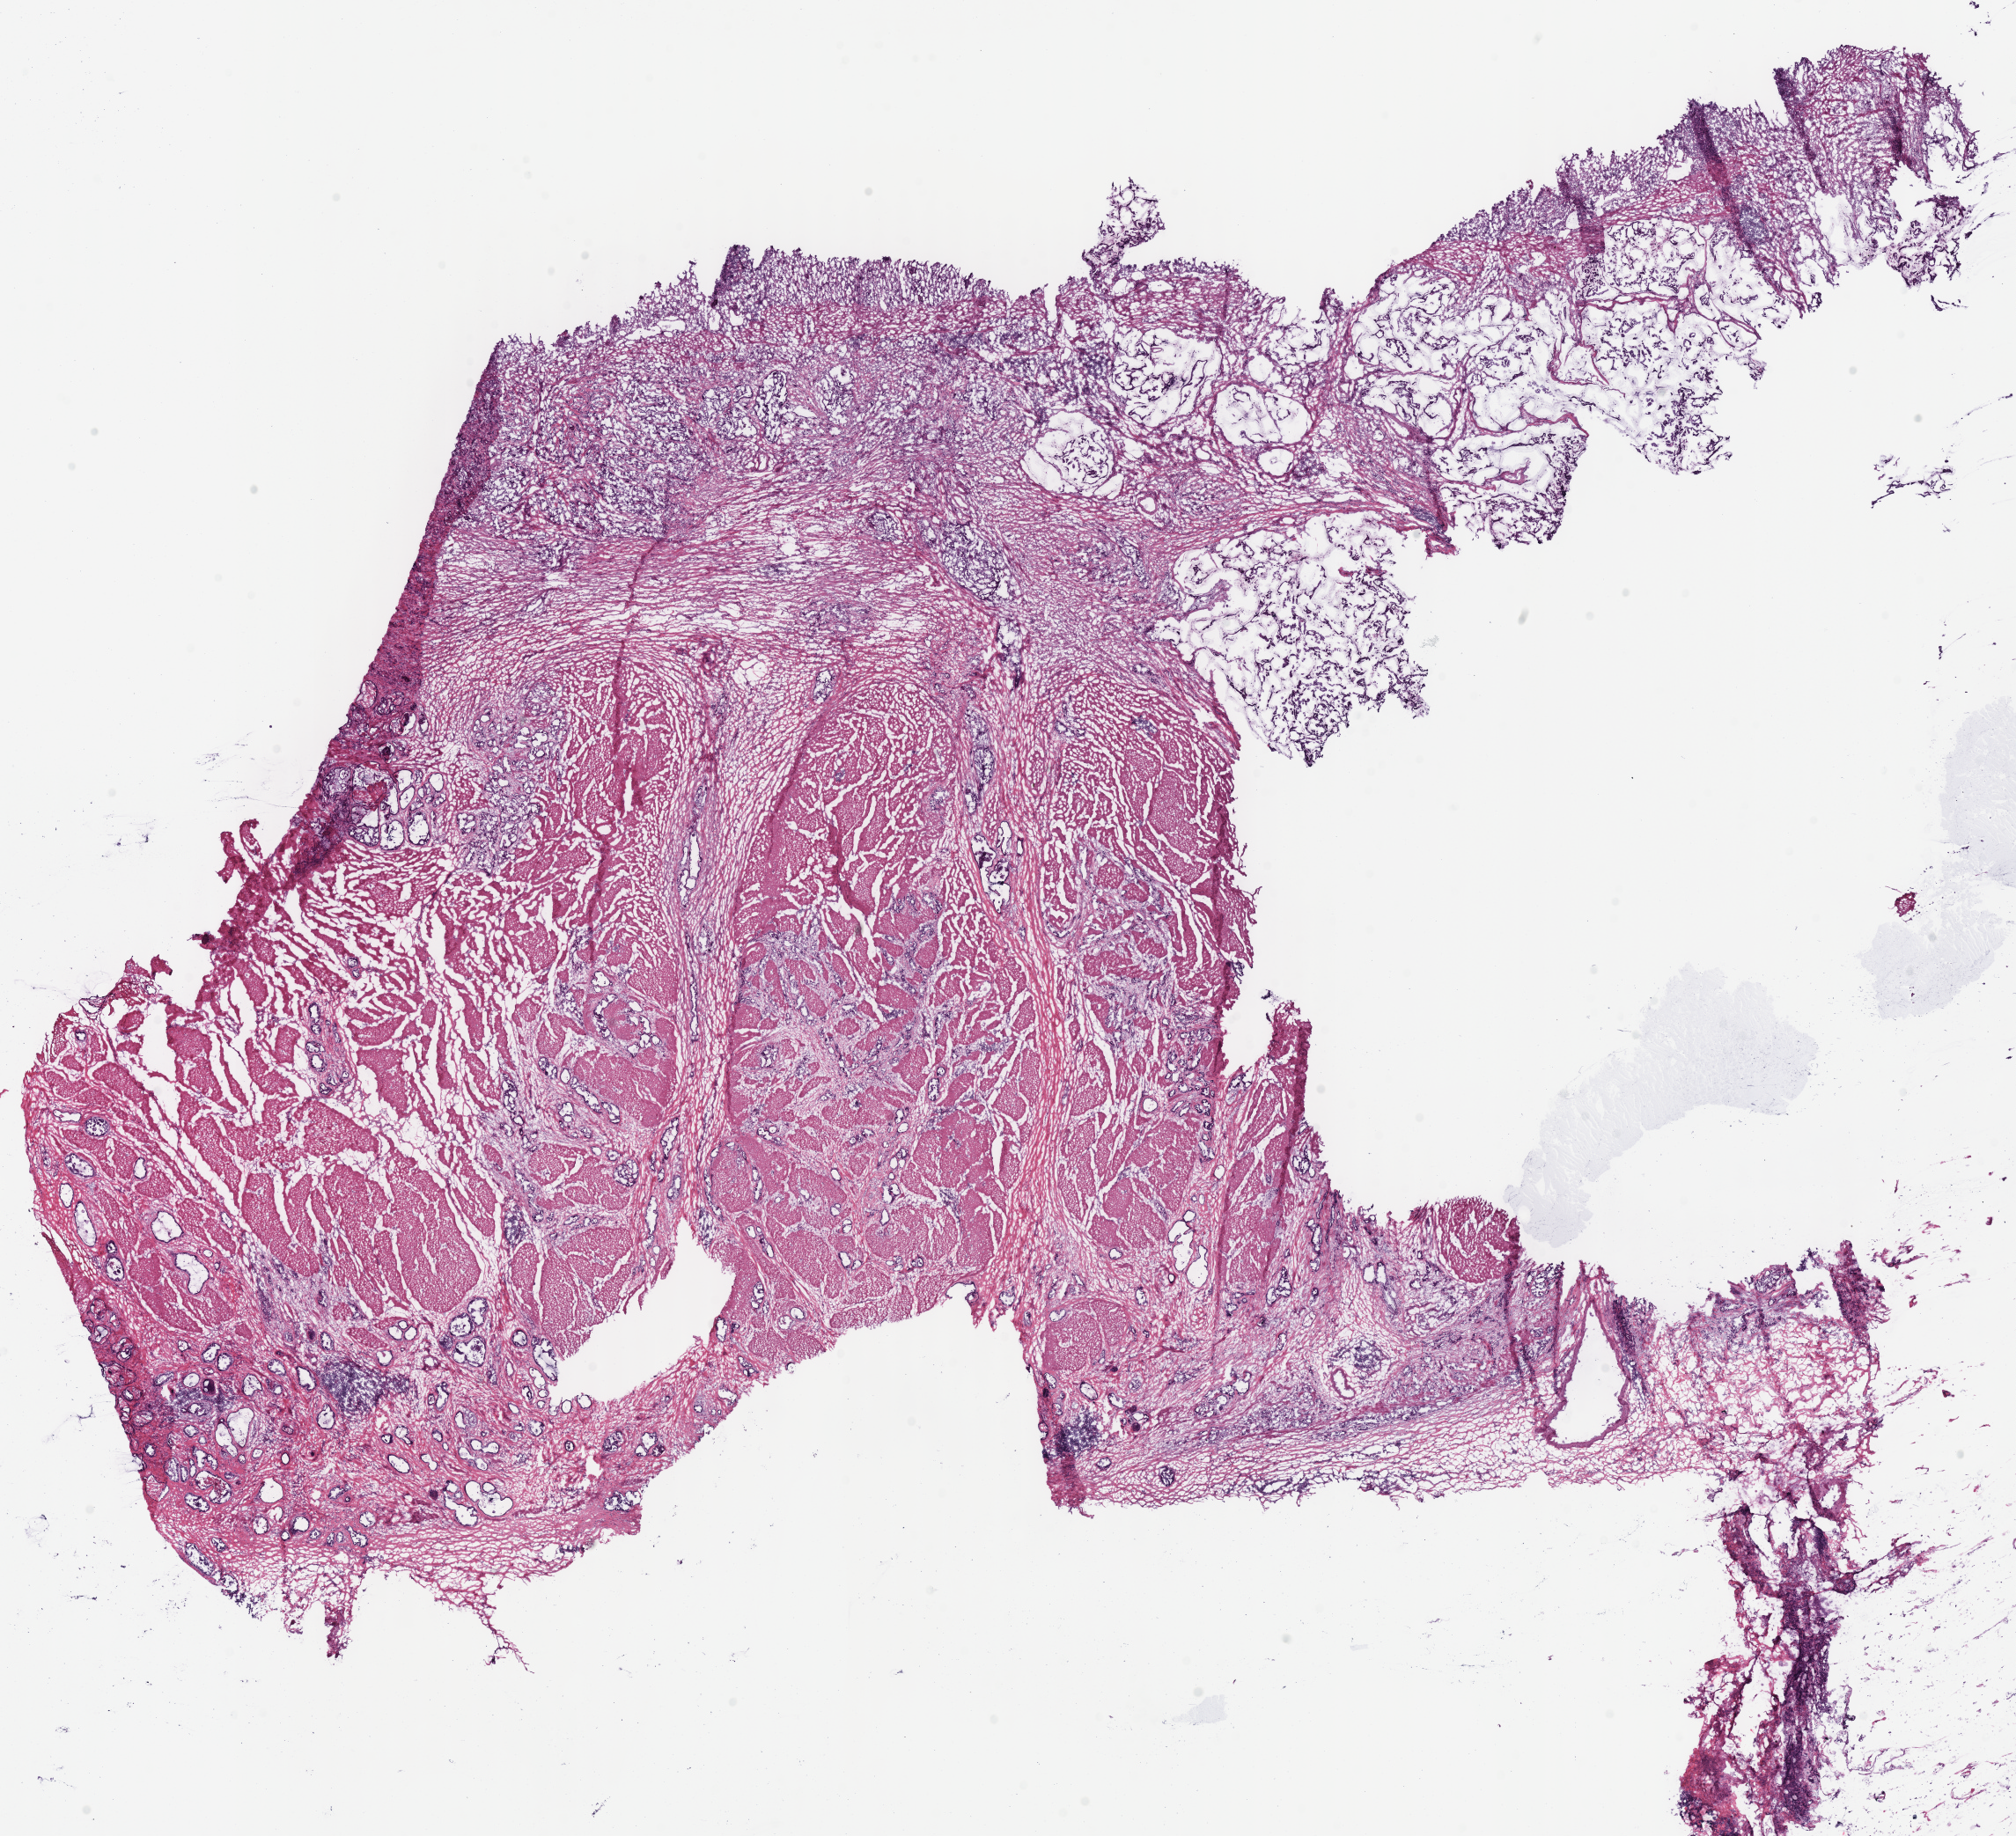
Whole-slide histology image, H&E — whole scanned area (about 18.0 x 16.4 mm, acquisition: 40x scan) shown as a low-resolution overview, frozen section from the bottom of the tissue portion, sample: primary tumour, stomach. Patient: female, age at initial diagnosis 76 years. Composition of this section per pathologist review: tumour cells 80%, tumour nuclei 75%.
Pathologic diagnosis: Adenocarcinoma, NOS (fundus of stomach).